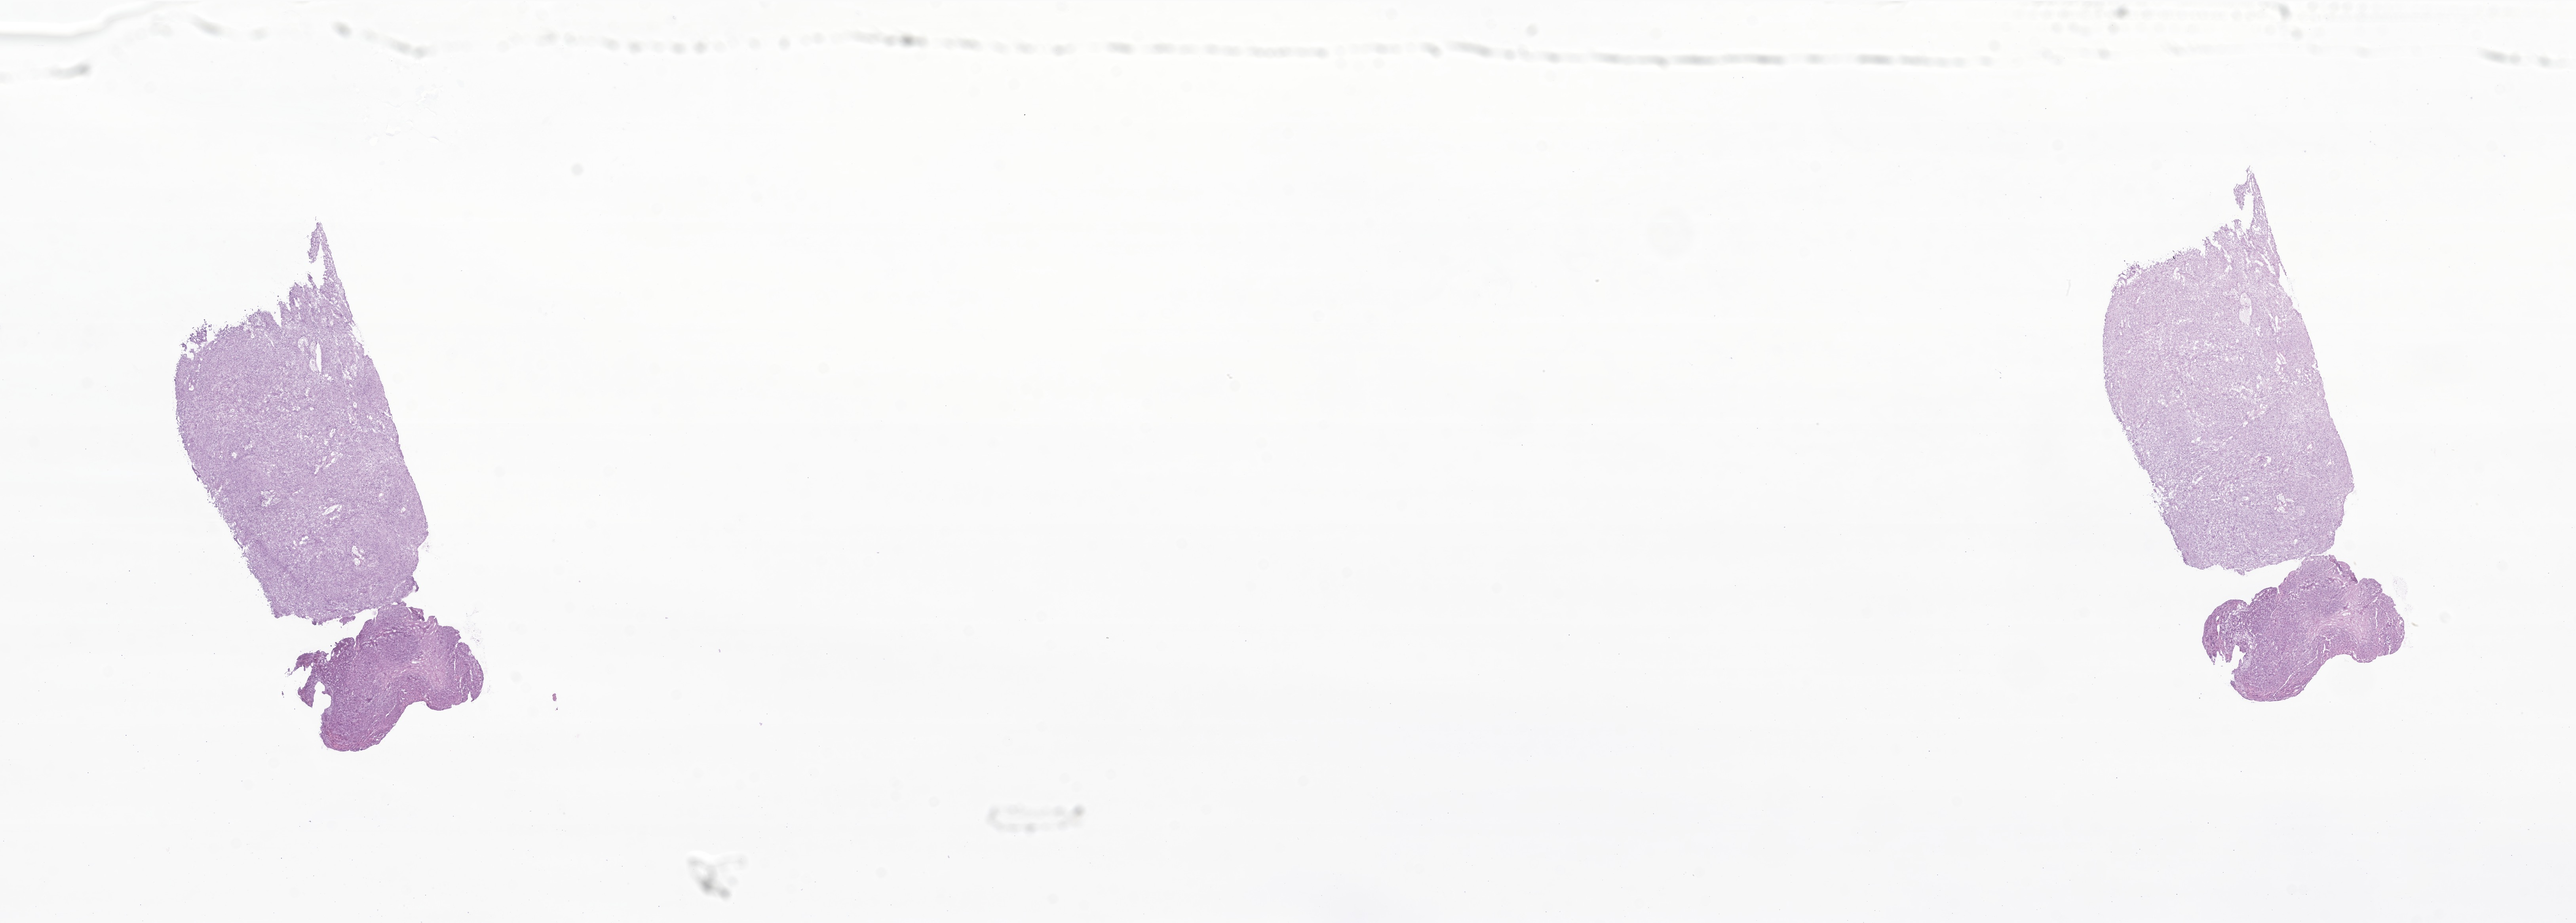
Digitized hematoxylin and eosin (H&E)-stained section of tumor tissue from the brain — a low-resolution overview of the entire scanned area, about 27.4 x 9.8 mm; frozen section (OCT-embedded). Patient male; age 161 months (13 years 5 months).
• recorded diagnosis: Schwannoma, NOS